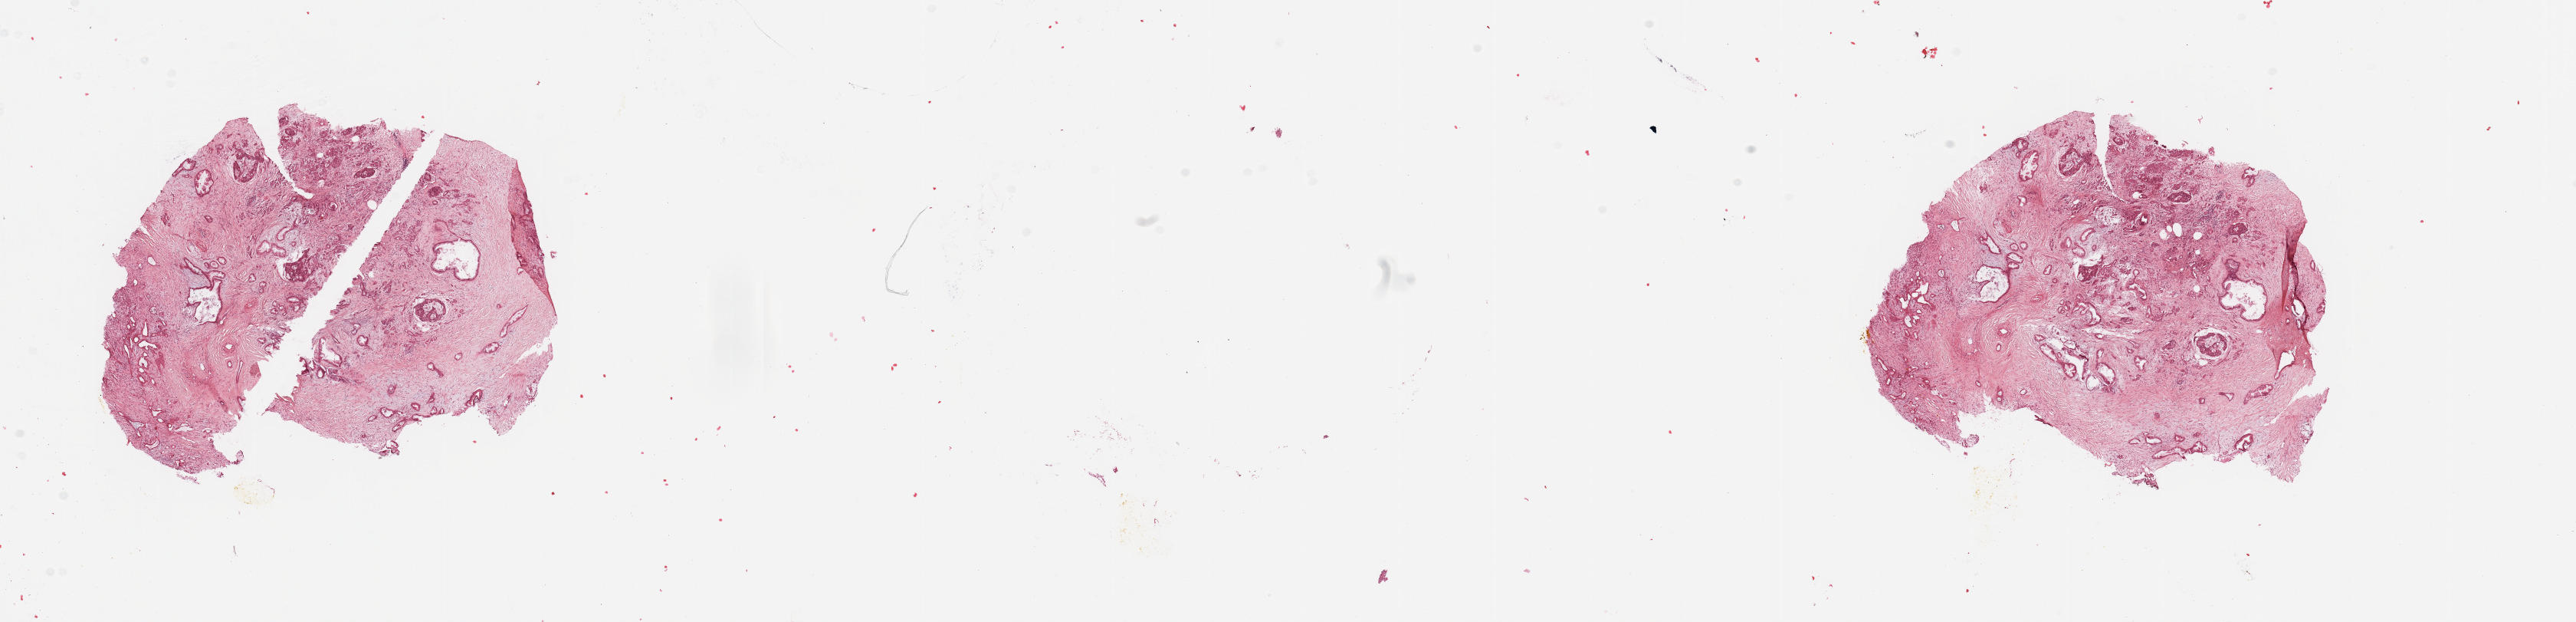
Digitized H&E-stained tissue section (whole slide), shown as a low-resolution overview of the whole scanned area (about 26.6 x 6.4 mm), pancreas, tumour tissue. 69-year-old male patient. Histologic grade: G3 (poorly differentiated).
* AJCC pathologic stage: IIB
* histologic diagnosis: Infiltrating duct carcinoma, NOS
* primary tumour site (as recorded): head